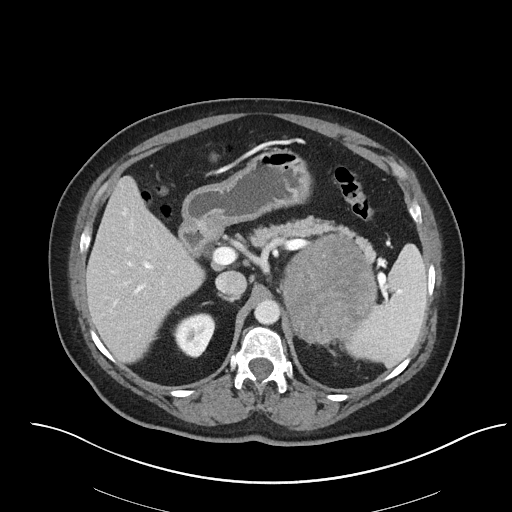
Contrast-enhanced abdominal CT, one axial slice. Slice 52 of 92 in the series (ordered by position). Reconstruction kernel I40f/2. 120 kVp. Soft-tissue window (W 400 / L 40 HU). 3 mm slice thickness. 512 × 512 image matrix, field of view 440 × 440 mm. Patient: female, 53 years. From the clinical record (not read from this slice): diagnosis: adrenocortical carcinoma; tumour side: left adrenal; tumour size at pathology: 9 cm; Ki-67 index: 28 %; stage (as recorded): 2.
Outlined on this slice (semi-automatically segmented with operator editing):
- mass: bounding box <283,236,376,342> (left, top, right, bottom; pixels)